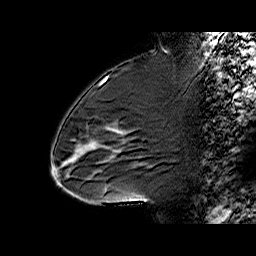
Breast MRI (dynamic contrast-enhanced), one sagittal slice. Dynamic contrast-enhanced series, time point 2 of 6 at this slice position (early post-contrast). 1.5 T. TE 6.3 ms, TR 32.4 ms. 256 × 256 image matrix, field of view 200 × 200 mm. Female patient. From the clinical record (not read from this slice): setting: breast cancer imaged before/during neoadjuvant chemotherapy; receptor status: triple-negative.
Structures marked on this image (semi-automatically segmented with operator editing):
- analysis volume of interest (the breast-tissue region the enhancement analysis was run in; not a lesion): bounding box [x1, y1, x2, y2] px = [65, 88, 151, 187]
- tumour enhancement mask (voxels above the 100 % enhancement threshold inside the analysis volume of interest): [91, 131, 115, 145]